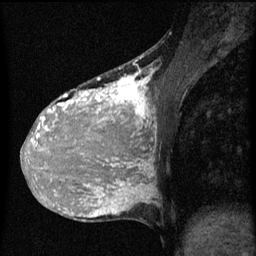
Breast MRI (dynamic contrast-enhanced), one sagittal slice; slice 23 of 60 in the series (ordered by position); dynamic contrast-enhanced series, image 2 of 3 at this slice position (ordered by acquisition); 1.5 T; TE 4.2 ms, TR 8 ms; 256 × 256 image matrix, field of view 180 × 180 mm. Female patient, age 36 years.
Annotated regions visible in this slice (semi-automatic segmentation, software-assisted and operator-edited):
- analysis volume of interest (the breast-tissue region the enhancement analysis was run in; not a lesion): bounding box [x1, y1, x2, y2] px = [32, 68, 161, 161]
- tumour enhancement mask (voxels above the 70 % enhancement threshold inside the analysis volume of interest): [32, 72, 153, 161]